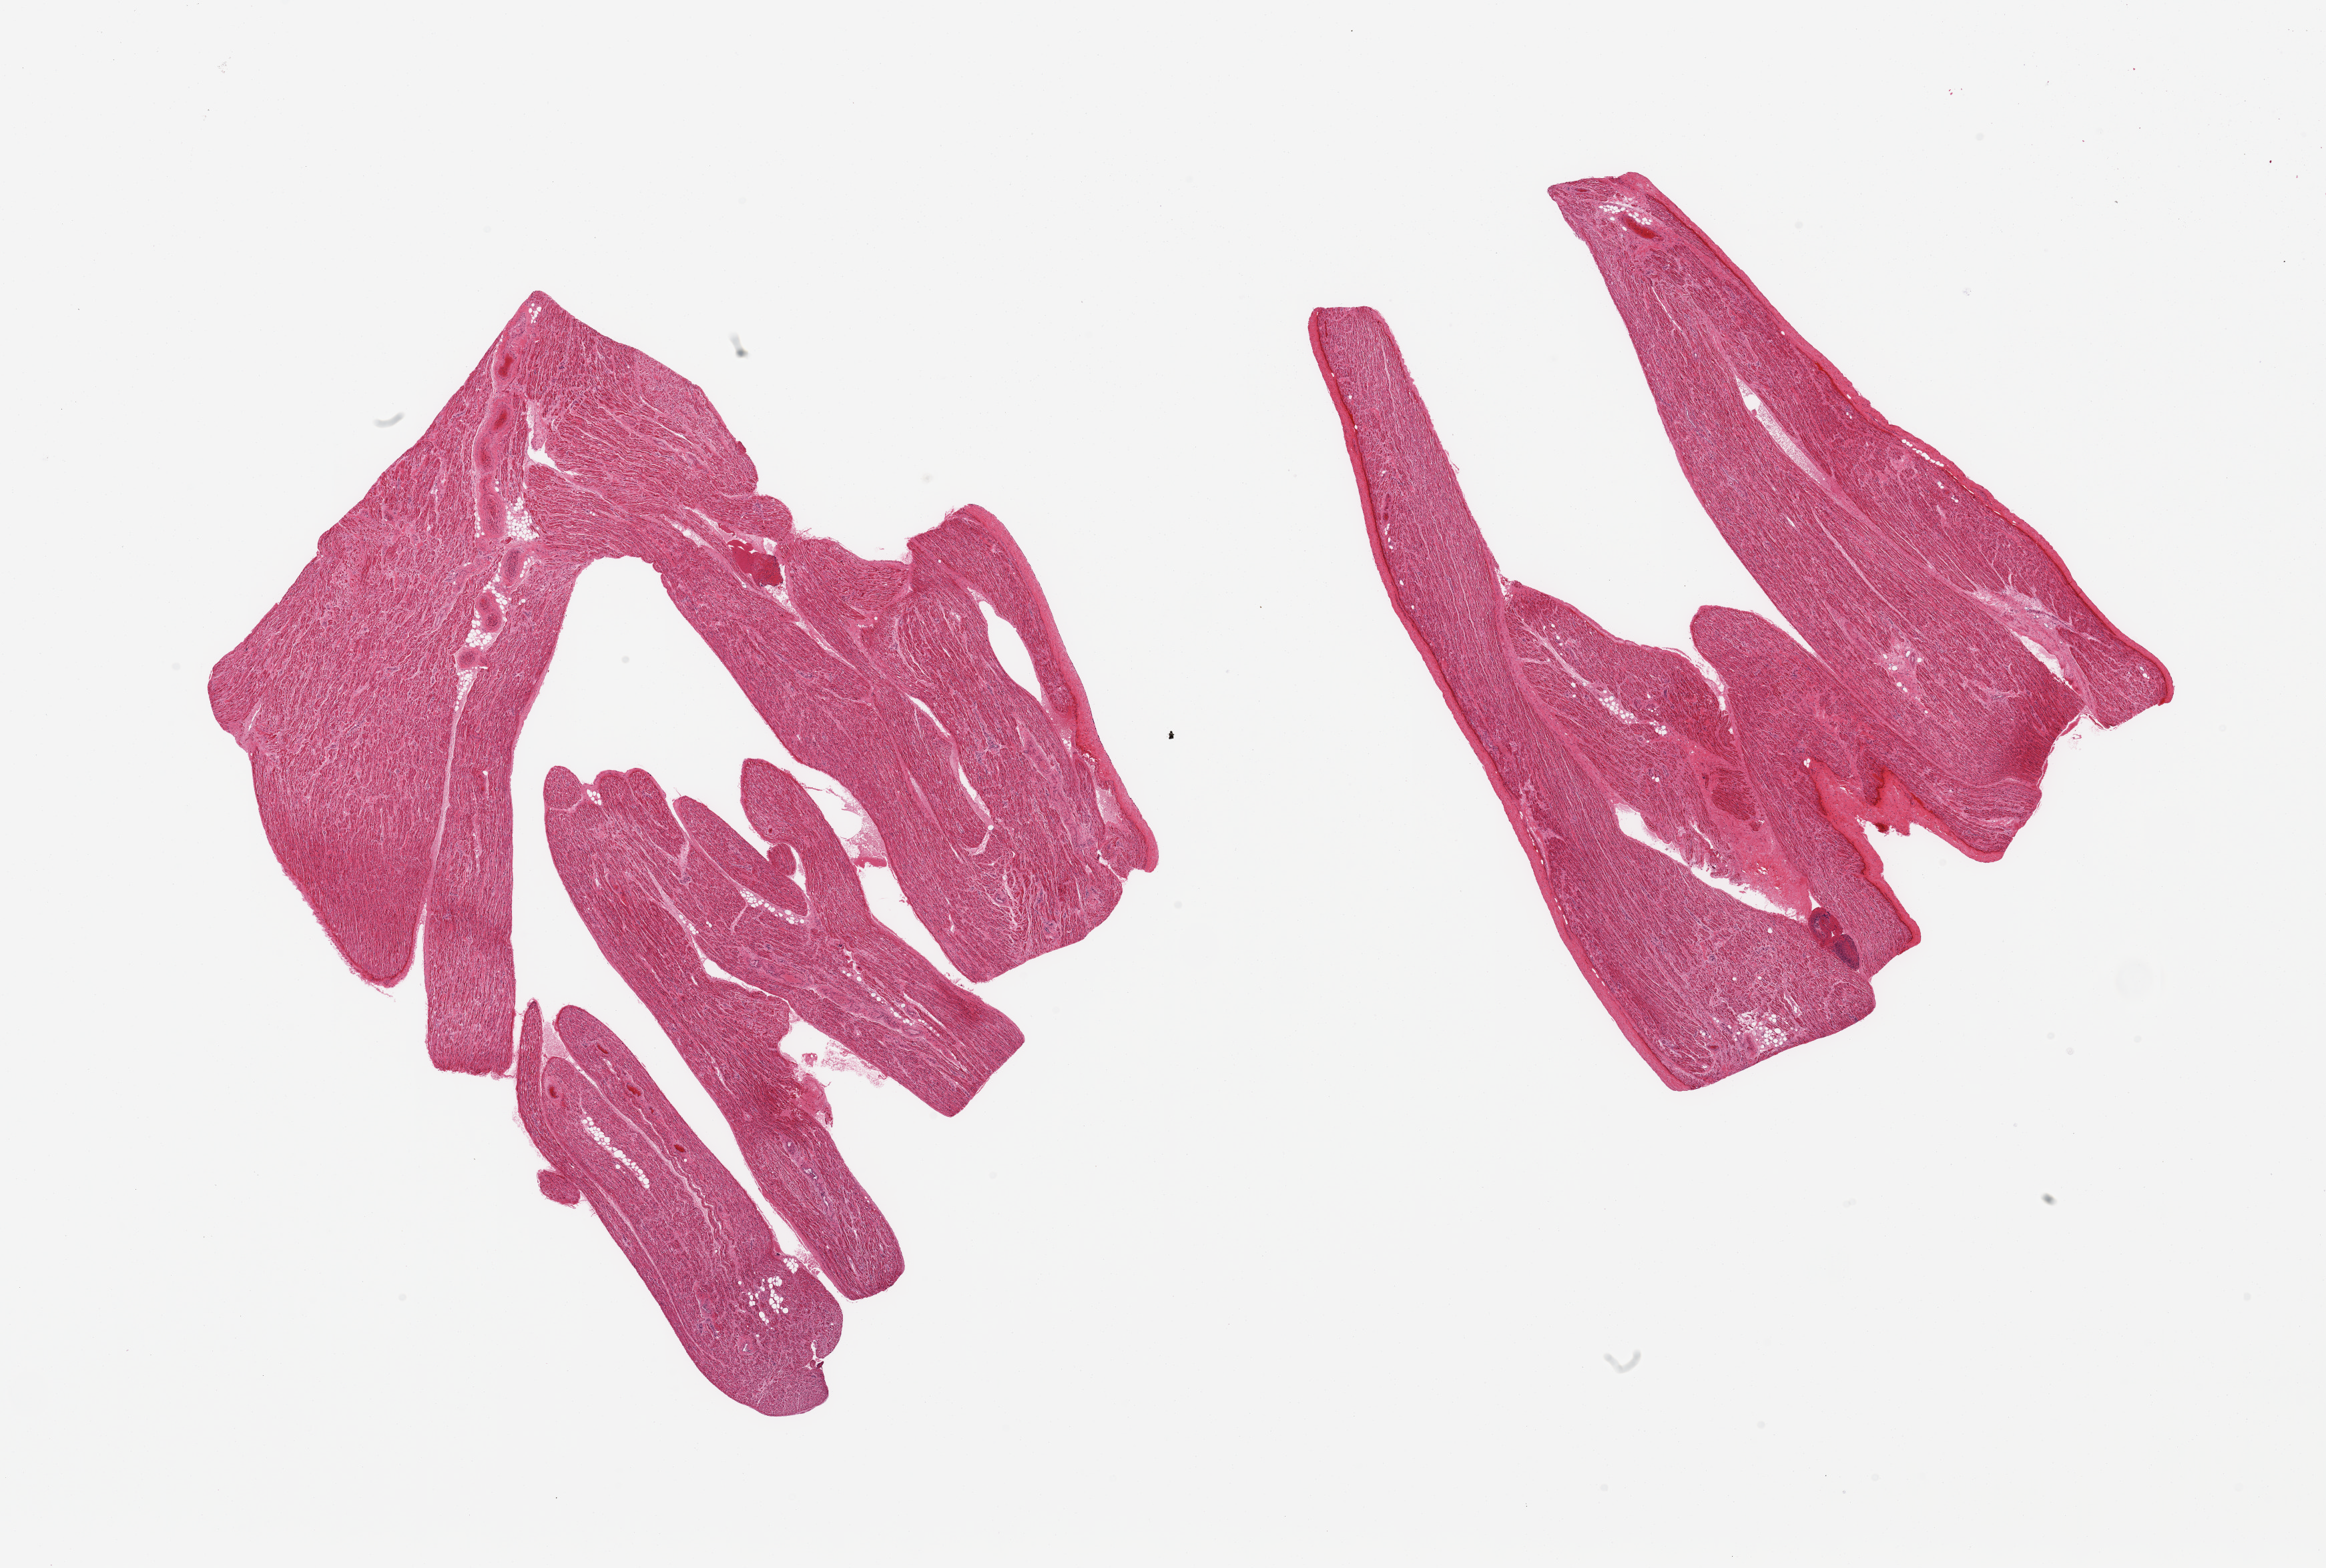
Whole-slide image, hematoxylin and eosin (H&E) stain, shown as a low-resolution overview of the whole scanned area (about 27.6 x 18.6 mm, slide scanned at 20x), PAXgene-fixed paraffin-embedded (PFPE) section, section of auricular appendage (target tissue), donor tissue sample. Donor sex: male.
• review note (as recorded): 2 pieces; no excess fat or fibrous stroma